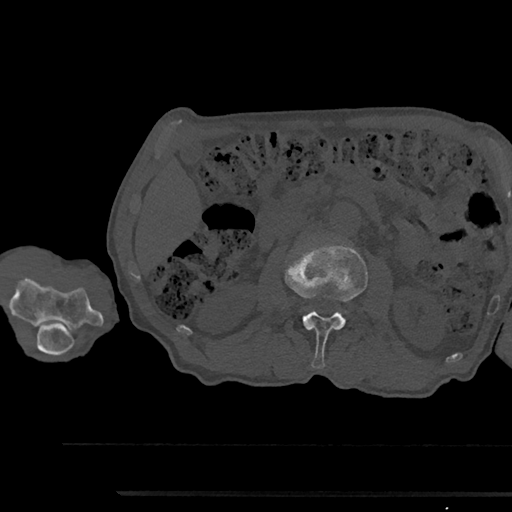
CT including the spine, one axial slice. Slice 550 of 797 in the series (ordered by position). Reconstruction kernel Br40s/3. Bone window (W 1800 / L 400 HU). 0.5 mm slice thickness. 512 × 512 image matrix, field of view 367 × 367 mm. Male patient, age 79 years. Case-level facts recorded for this patient, not image findings: primary cancer: prostate.
Outlined on this slice (semi-automatic segmentation, software-assisted and operator-edited):
- L2 vertebra: bounding box (x1, y1, x2, y2) in pixels: (285, 245, 367, 369)